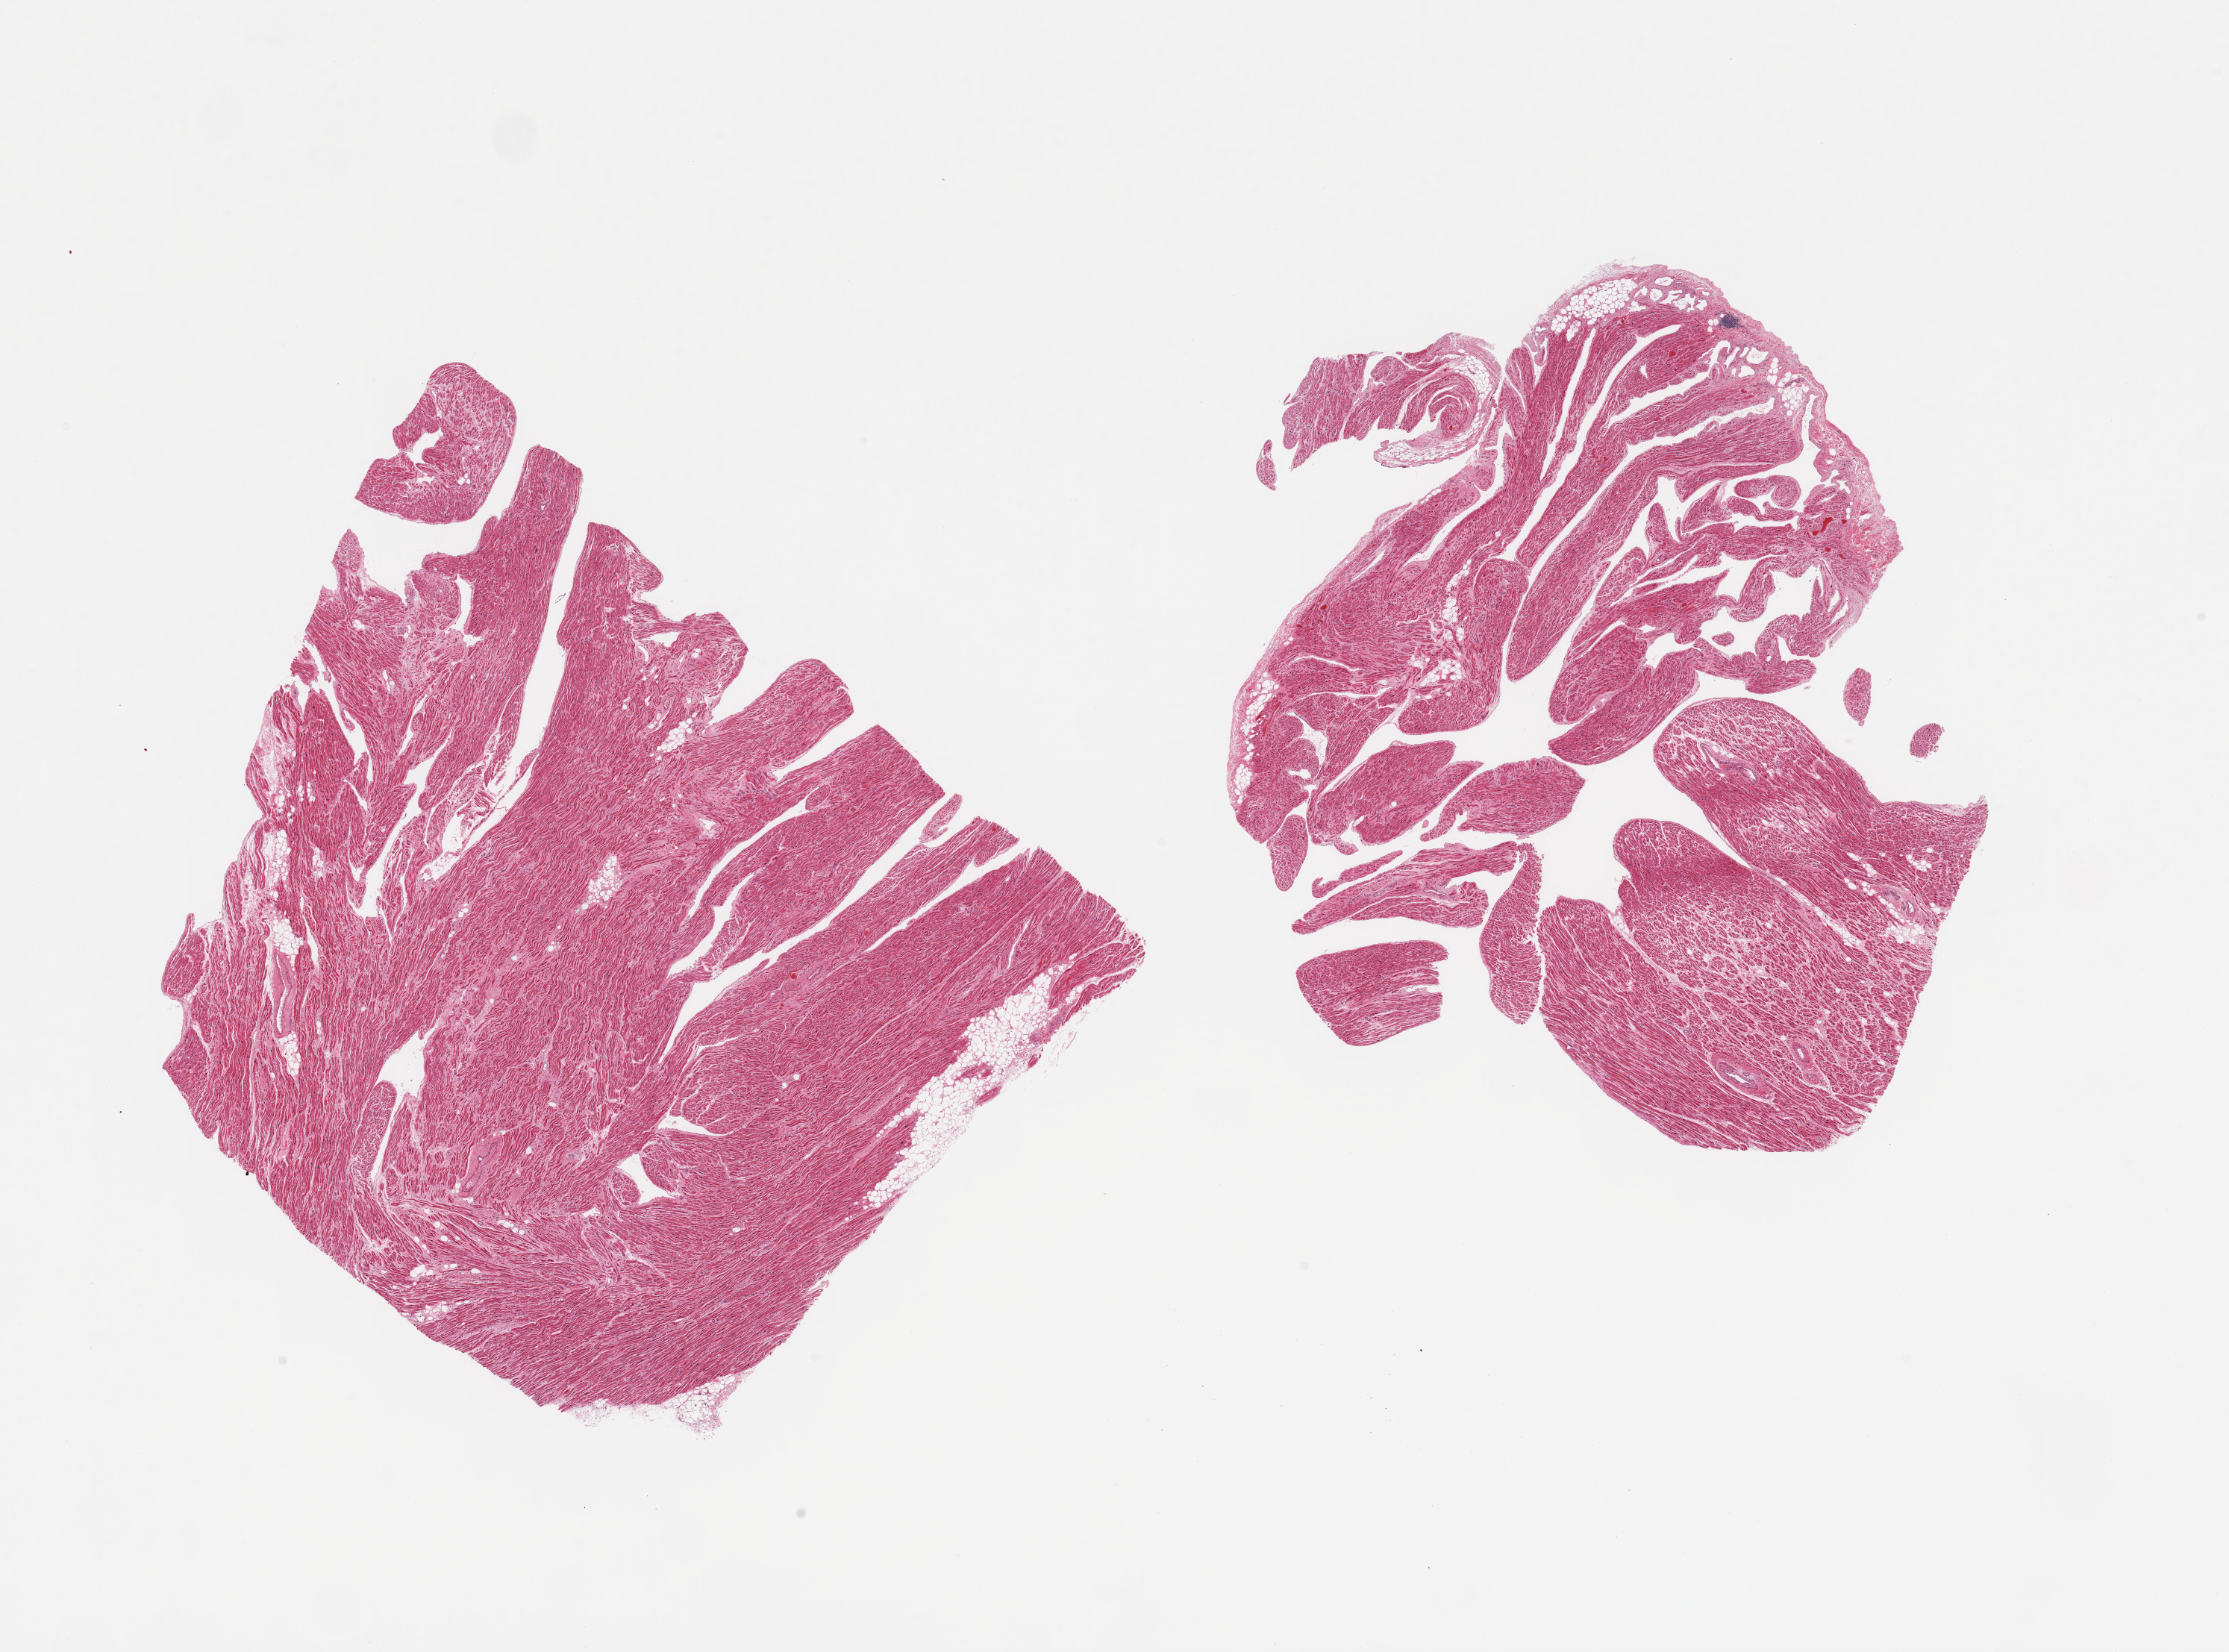
Digitized hematoxylin and eosin (H&E)-stained section, a low-resolution overview of the entire scanned area, about 23.6 x 17.5 mm. PAXgene-fixed, paraffin-embedded tissue. Sampled site (target tissue): auricular appendage. Tissue donor sample. Male donor.
* pathologist's review note for this sample: 2 pieces; <5% fat content